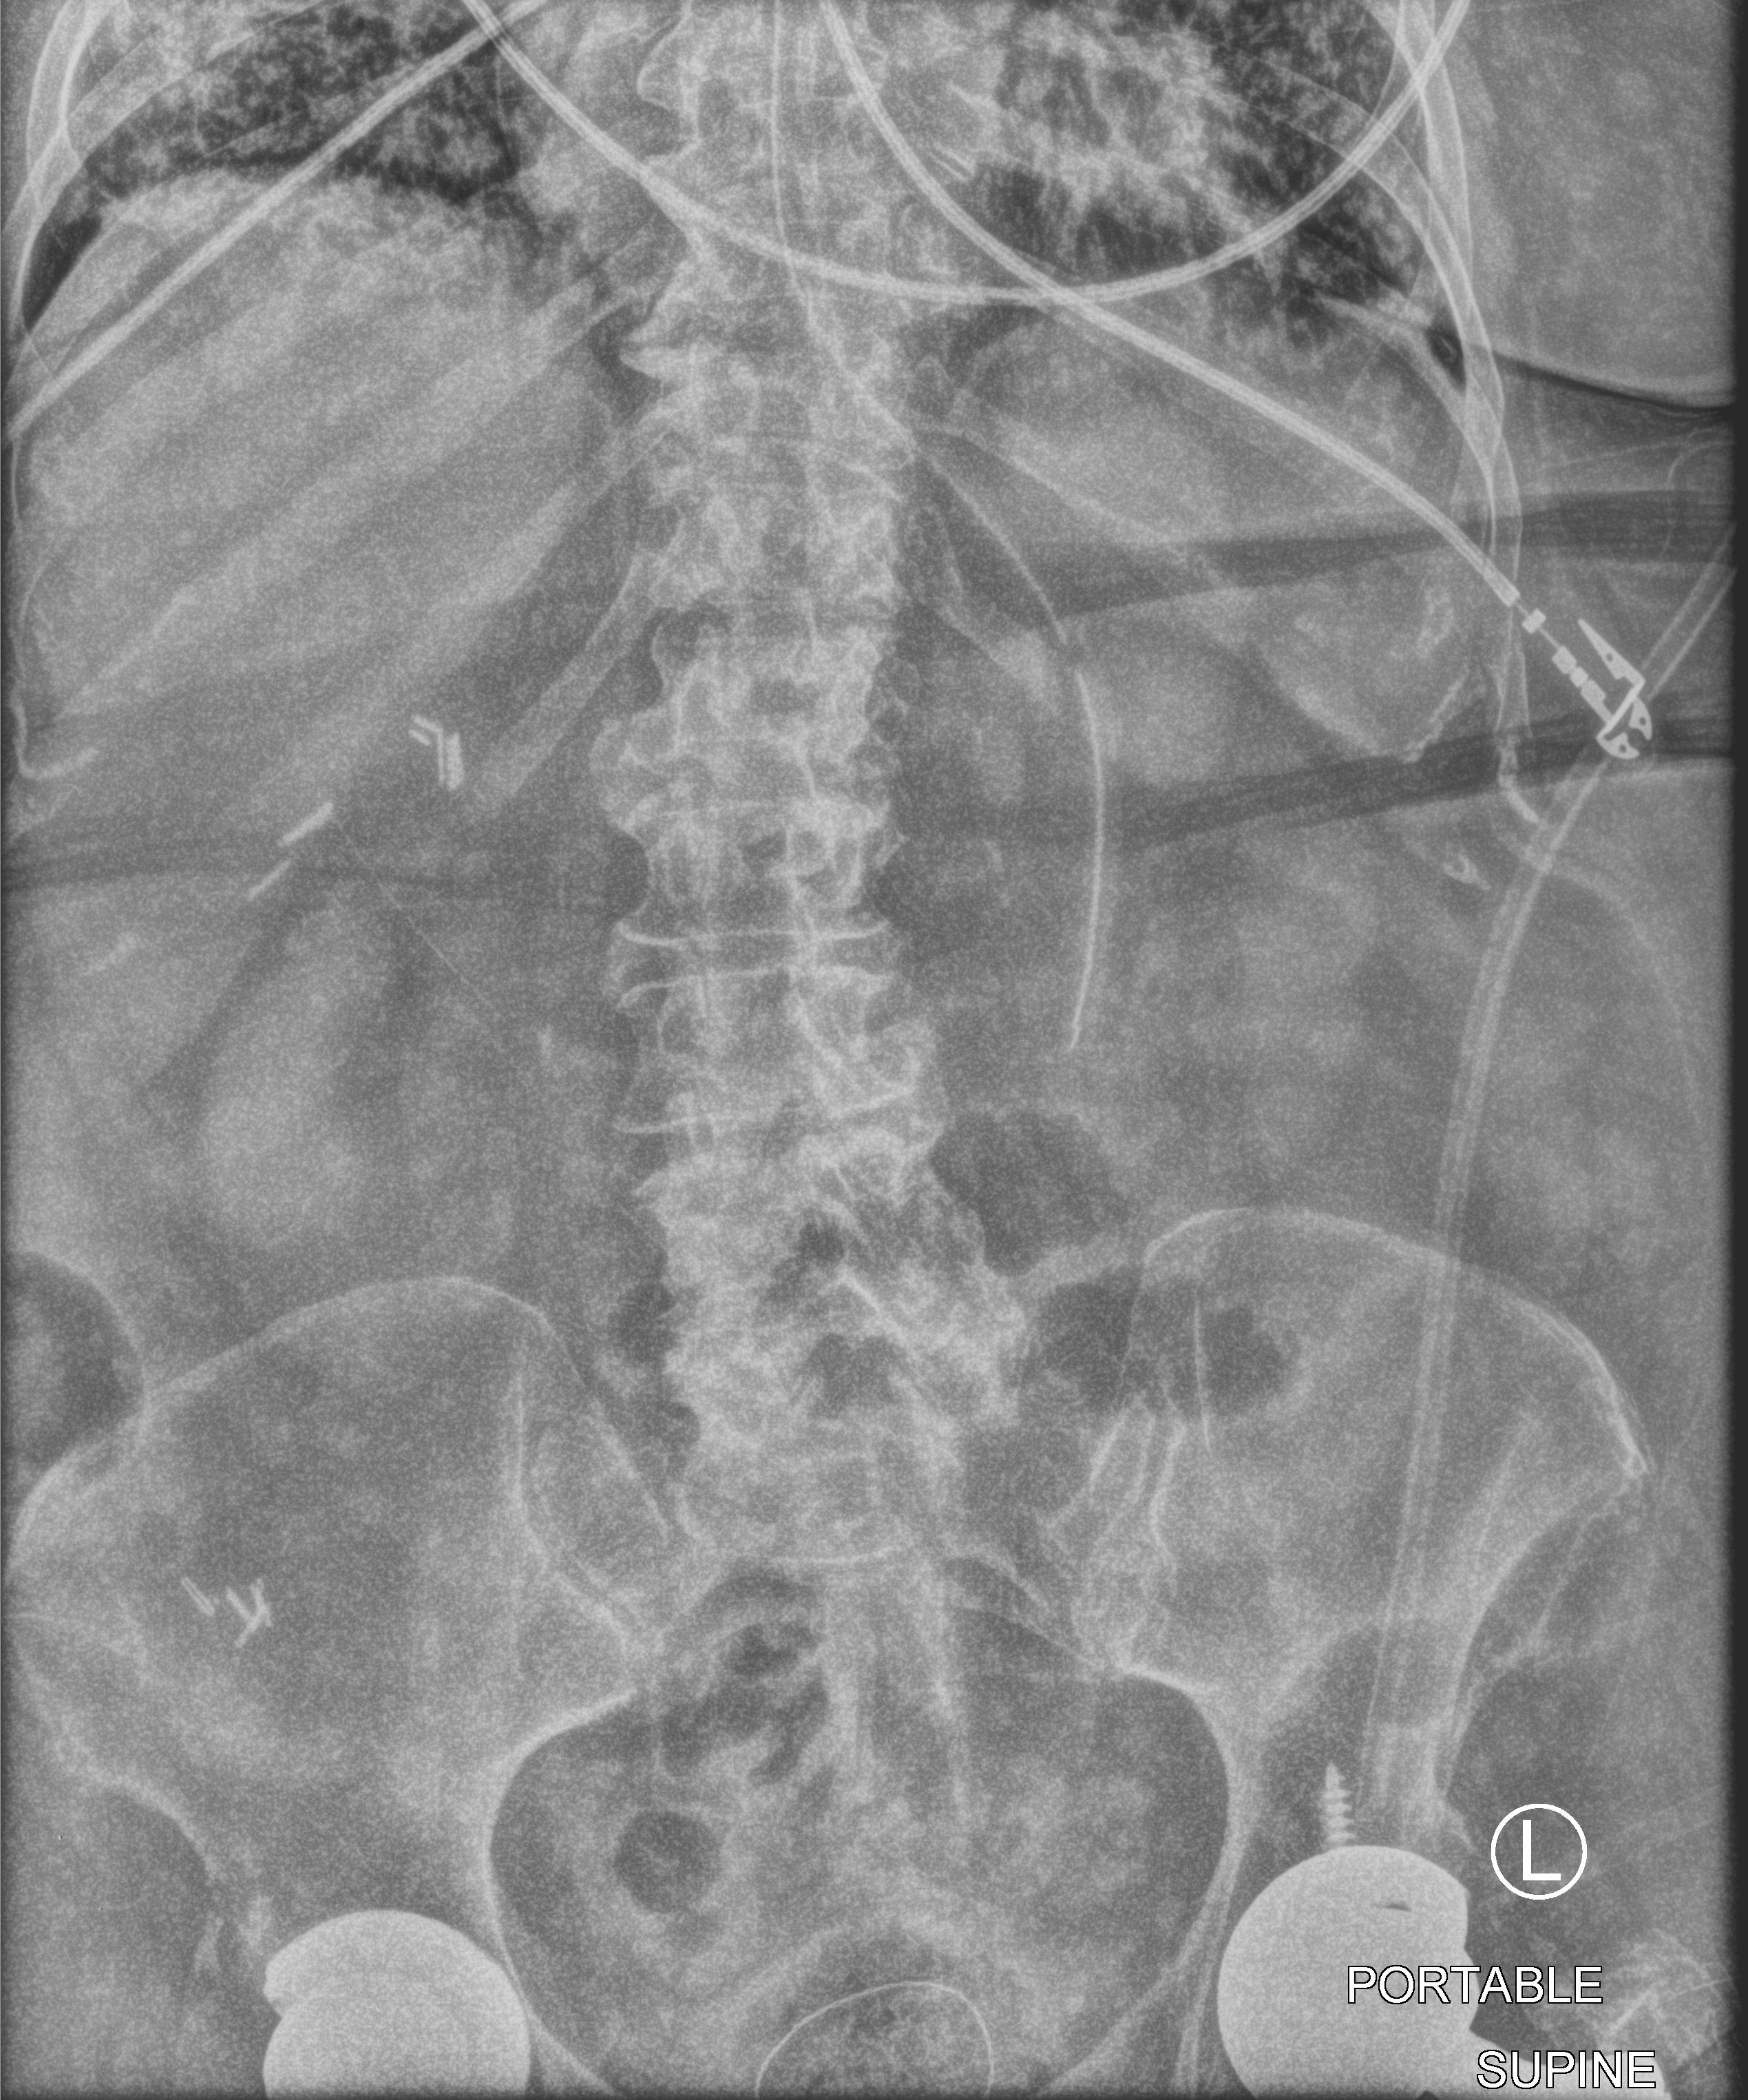
Bedside abdomen radiograph (computed radiography); anteroposterior (AP) projection. Female patient hospitalised with COVID-19, age 75–90 years.
Hospital-stay facts (about this admission, not read from this image; timing relative to this image not recorded):
- mechanically ventilated during this hospital stay: yes
- smoking status (admission record): former
- length of hospital stay: 56 days